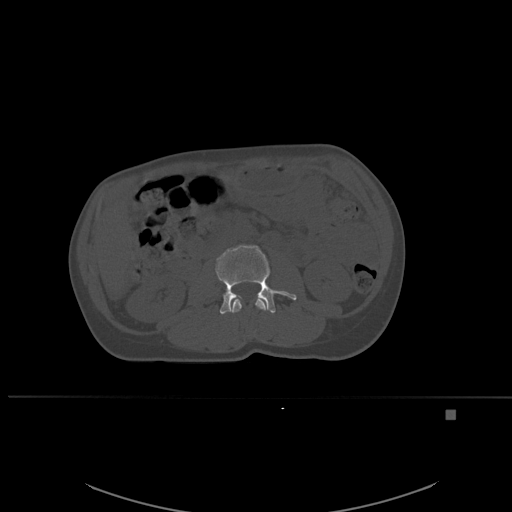
CT including the spine, one axial slice. Slice 221 of 537 in the series (ordered by position). Bone window (W 1800 / L 400 HU). 512 × 512 image matrix, field of view 440 × 440 mm. Patient: female, 45 years. Case-level facts recorded for this patient, not image findings: primary cancer: lung.
Annotated regions visible in this slice (semi-automatic segmentation, software-assisted and operator-edited):
- L2 vertebra: bounding box [x1, y1, x2, y2] px = [231, 296, 268, 313]
- L3 vertebra: [215, 245, 297, 314]